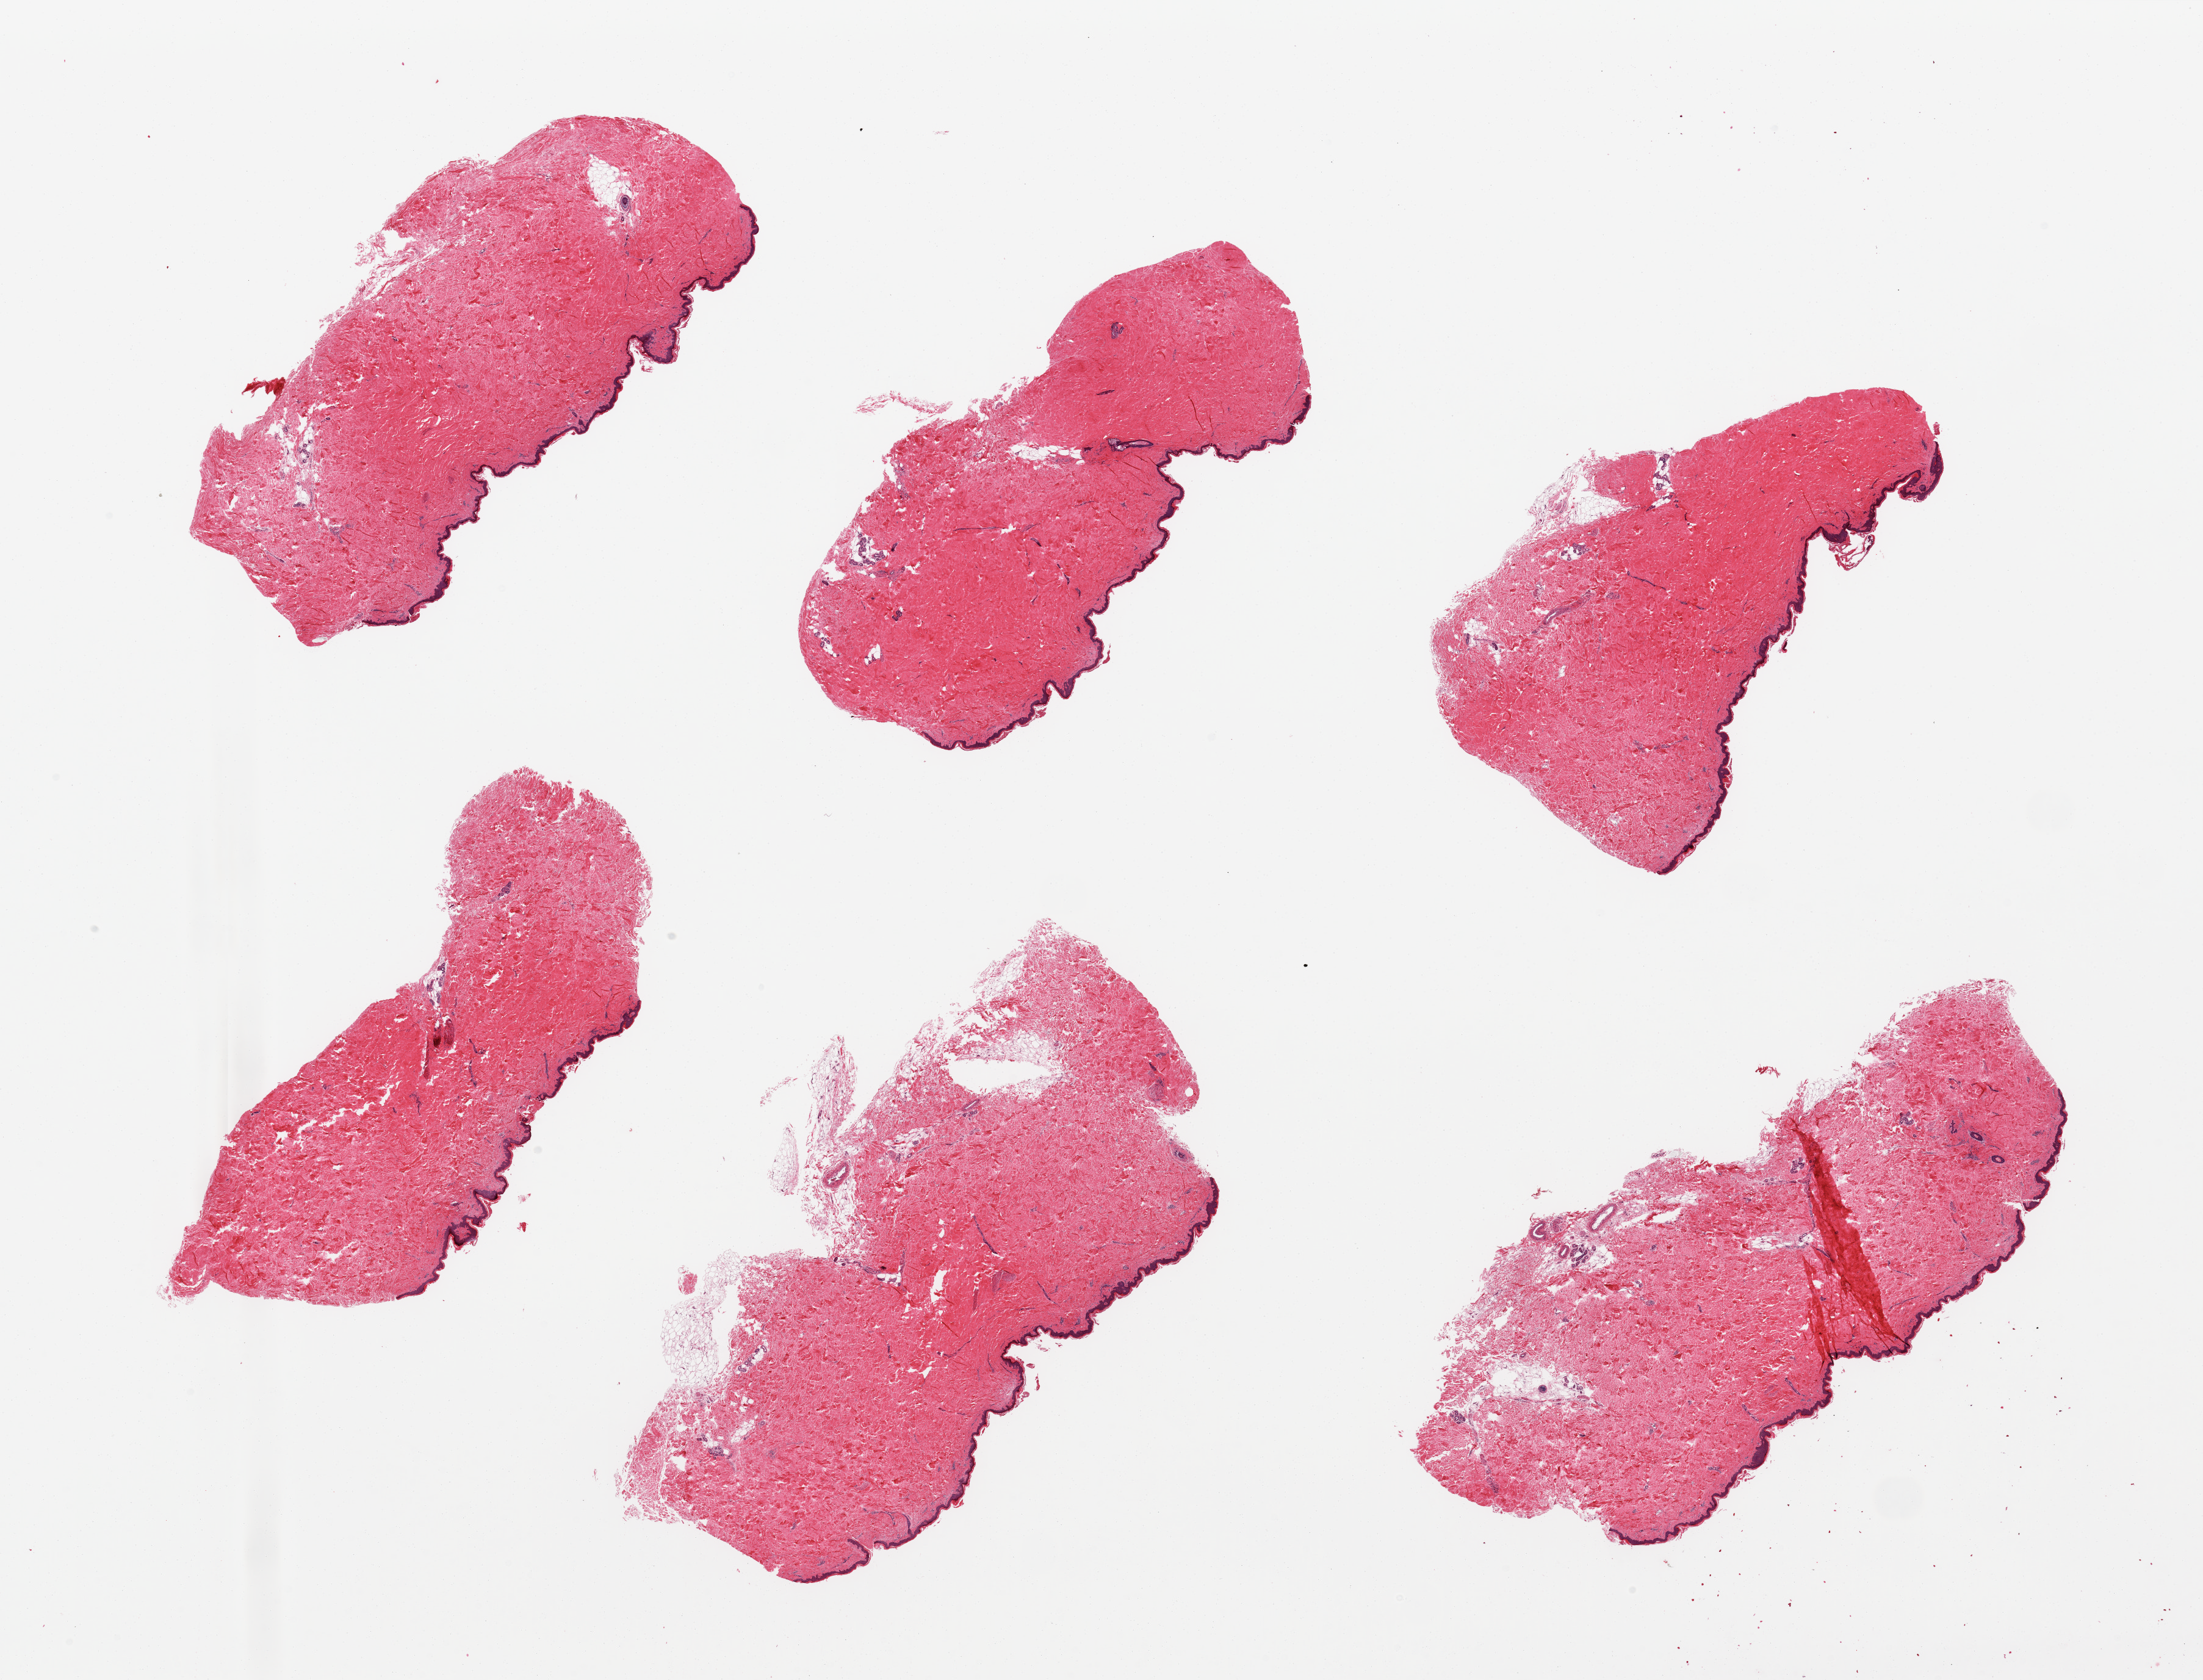
Whole-slide image, H&E stain, brightfield, low-resolution overview of the scanned area, about 28.5 x 21.8 mm. PAXgene-fixed, paraffin-embedded tissue. Section of skin of suprapubic region (target tissue). Donor tissue sample. Donor sex: female.
Review note (as recorded): 6 pieces, no dermal fat; squamous epithelium is ~50-60 microns.